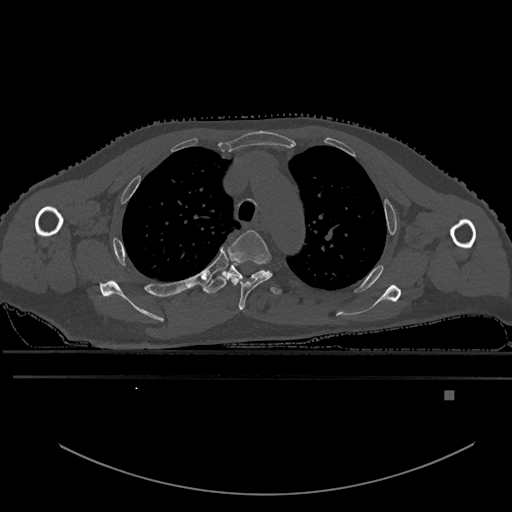
CT including the spine, one axial slice; slice 432 of 969 in the series (ordered by position); bone window (W 1800 / L 400 HU); 512 × 512 image matrix, field of view 456 × 456 mm. Male patient, age 82 years. Case-level facts recorded for this patient, not image findings: primary cancer: prostate; vertebrae with lytic lesions (as recorded): T11, T9, T8, T2.
Structures marked on this image (semi-automatically segmented with operator editing):
- T3 vertebra: bounding box (x1, y1, x2, y2) in pixels: (227, 230, 272, 310)
- T4 vertebra: (203, 263, 282, 295)